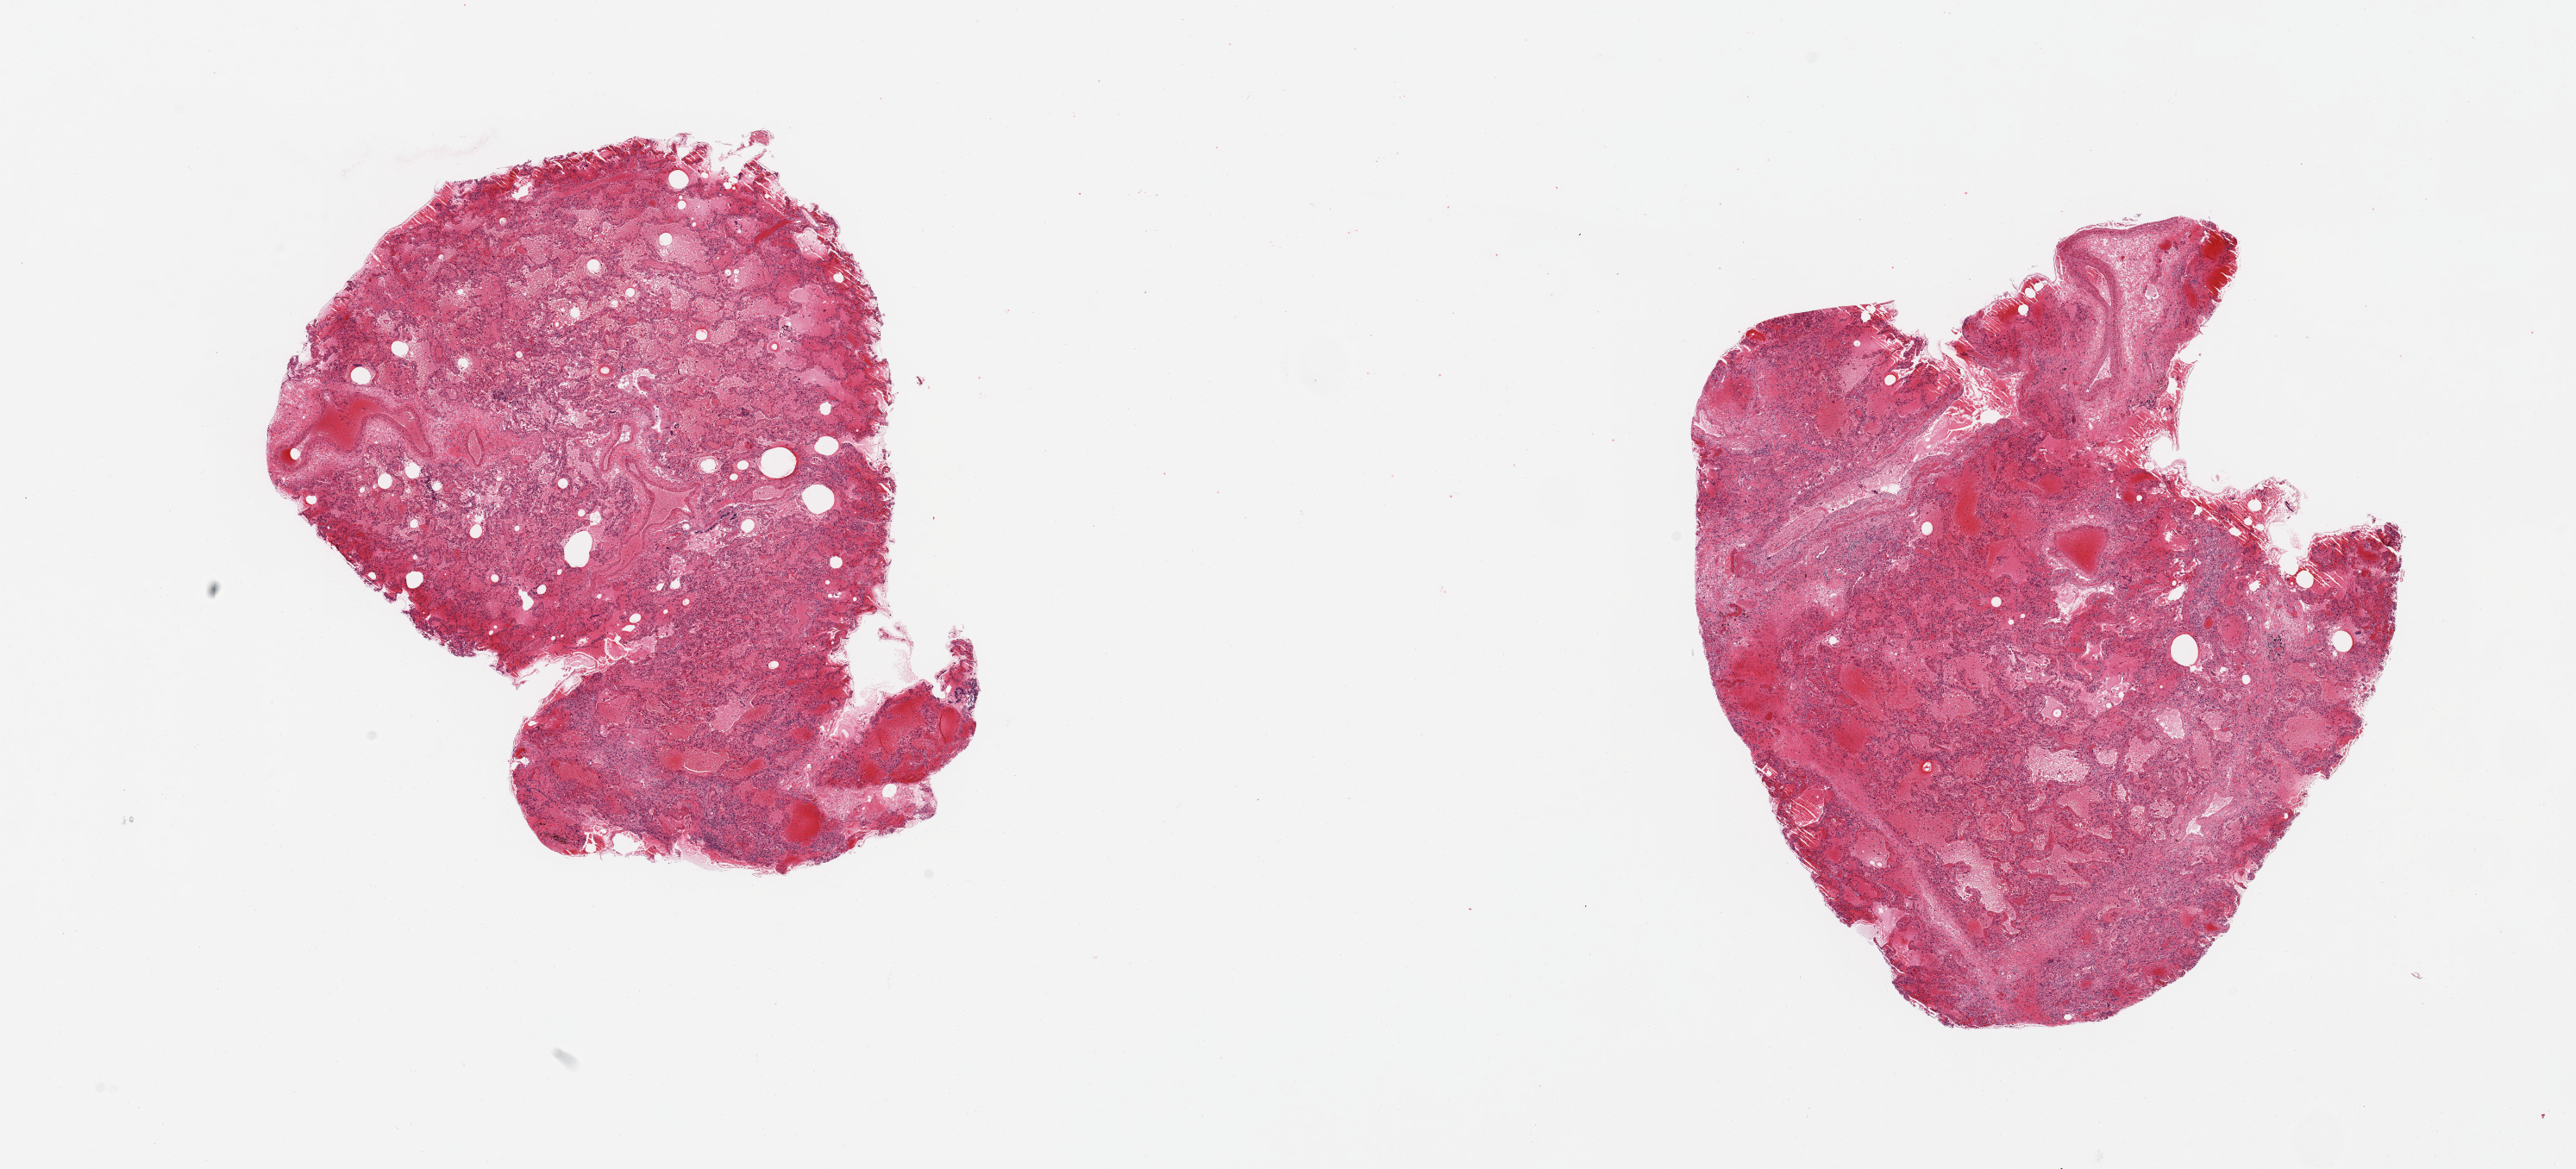
Digitized haematoxylin and eosin-stained section — low-resolution overview of the scanned area, about 23.6 x 10.7 mm; PAXgene-fixed paraffin-embedded (PFPE) section; sampled site (target tissue): lung; donor tissue sample. Donor: male.
Pathologist's review note for this sample: 2 pieces; hemorrhage, edema, fibrosis.